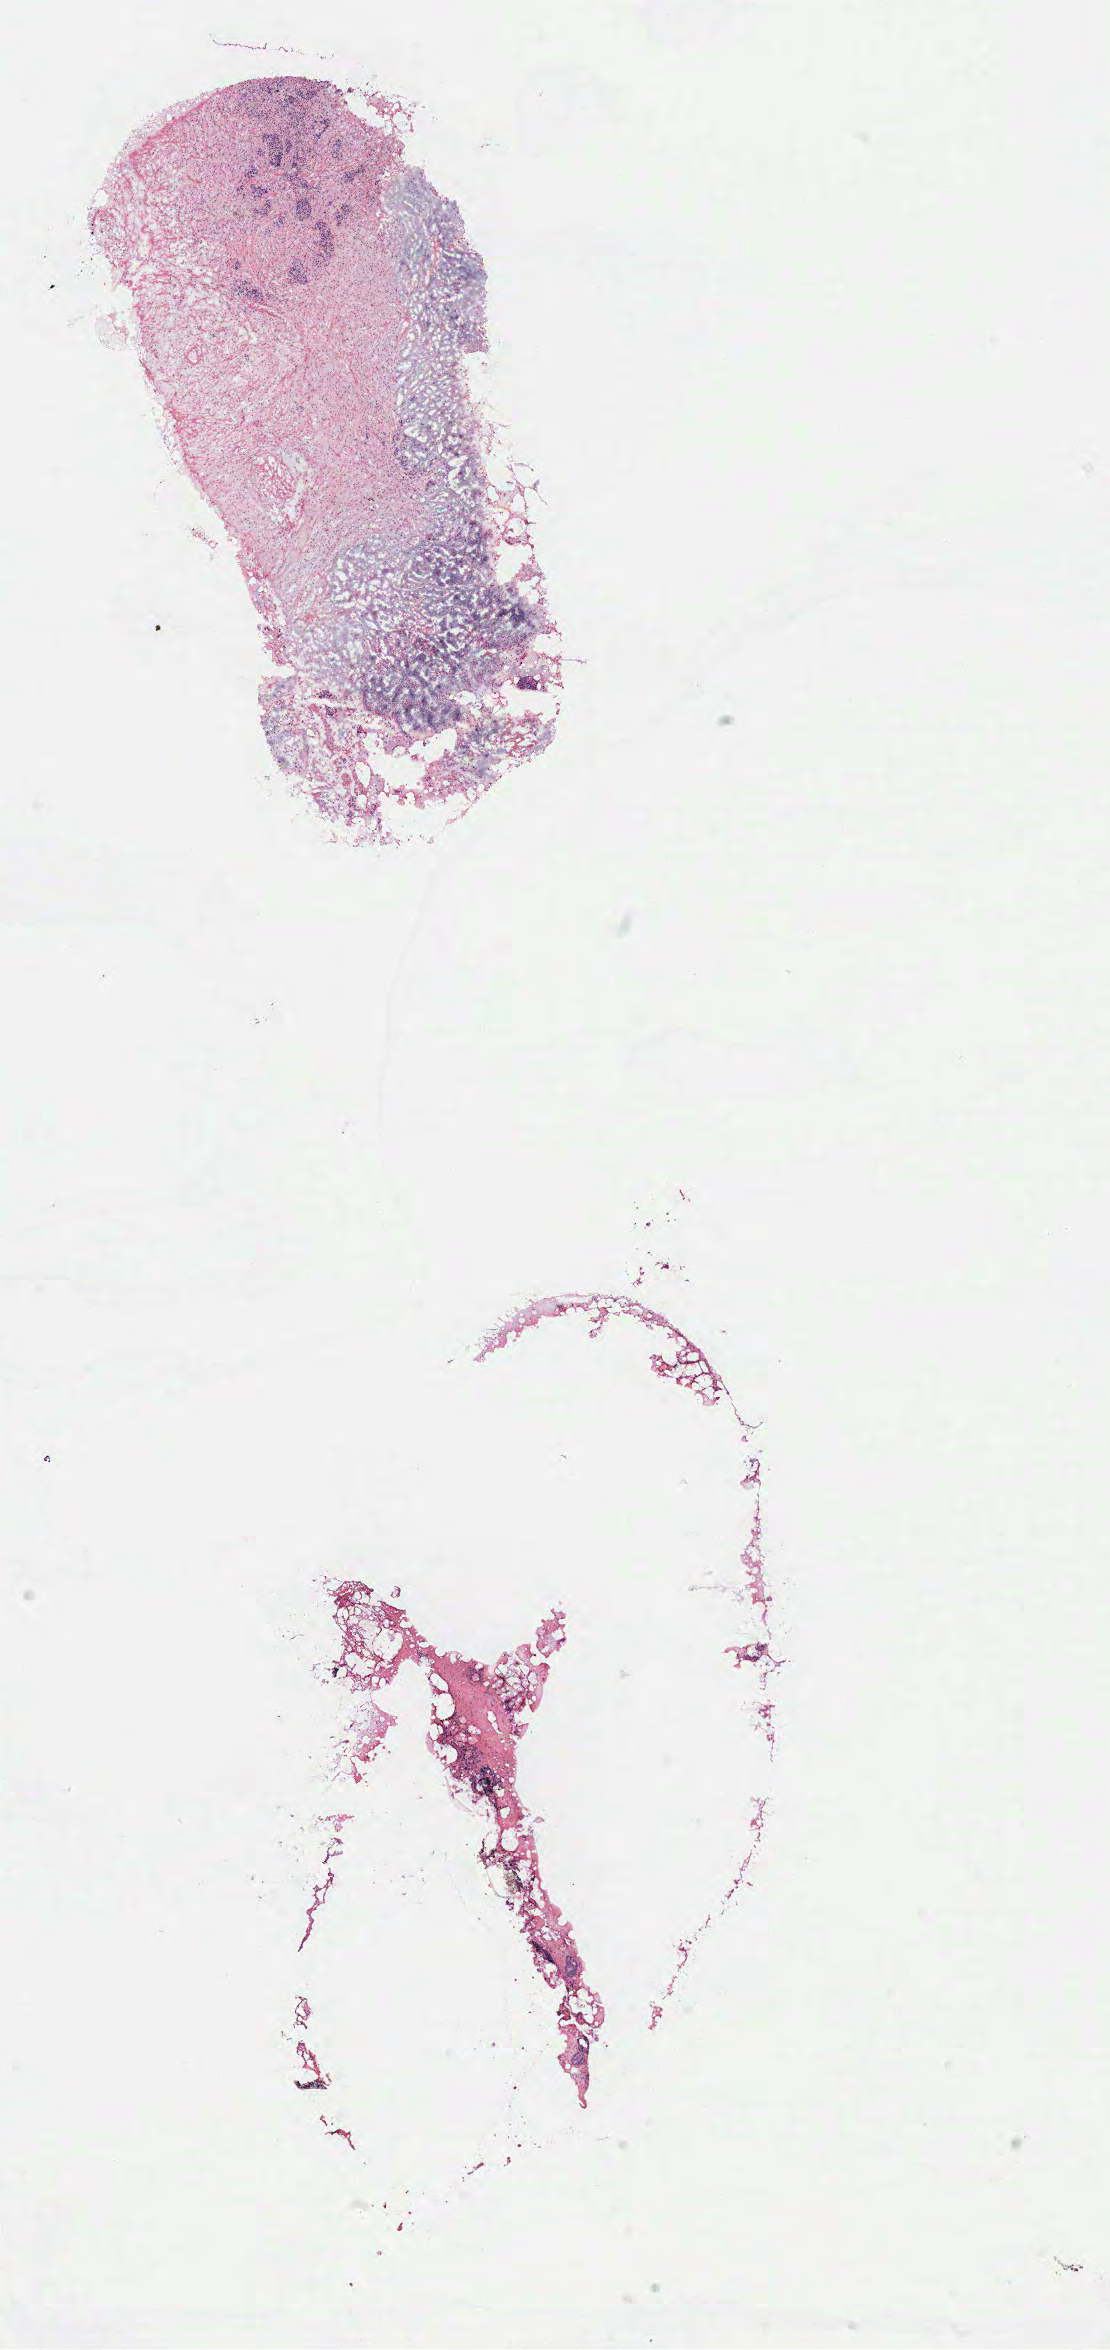
Digitized Hematoxylin and eosin (H&E) stained tissue section (whole slide), shown as a low-resolution overview of the whole scanned area (about 8.9 x 18.8 mm, acquisition: 40x scan). Female, 64 y/o.
Specimen: breast, tumour tissue.